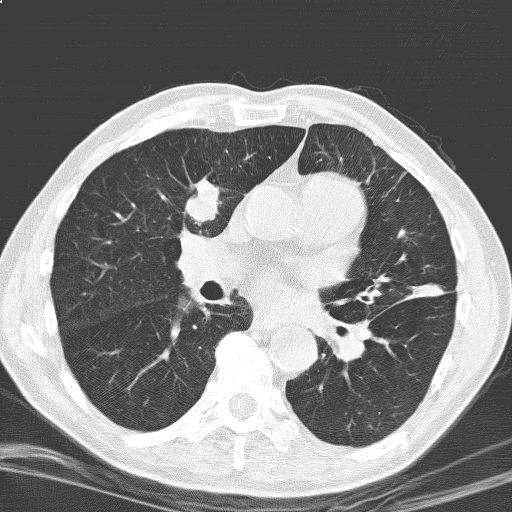
Low-dose screening chest CT, one axial slice. Position 97 of 184 along the scan axis. 120 kVp. Lung window (W 1500 / L -600 HU). 512 × 512 image matrix, field of view 329 × 329 mm.
Outlined on this slice (expert manual segmentation):
- lesion 1 (tumor, upper lobe of right lung): bounding box (x1, y1, x2, y2) in pixels: (185, 179, 219, 223)